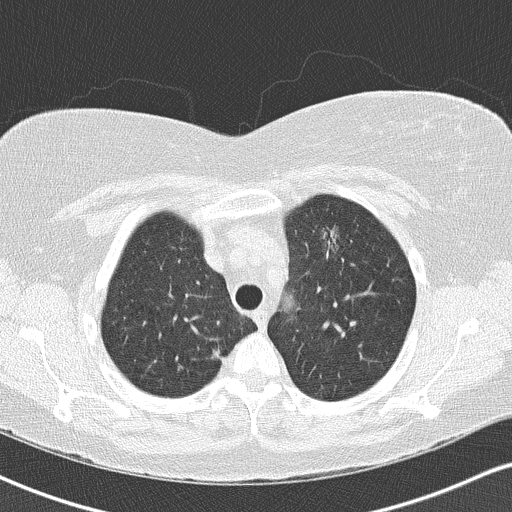
Low-dose screening chest CT, axial slice; second screening round (one year after baseline); lung window (W 1500 / L -600 HU); 120 kVp; slice 116 of 146 in the series. Female participant, aged 57 years at enrolment. Current smoker at enrolment.
Expert-annotated lung lesion, box from (x=311, y=219) to (x=352, y=264) px. The screening reader recorded 3 non-calcified nodules or masses ≥4 mm on this exam (left upper lobe, right upper lobe, right middle lobe); which of them this box marks is not recorded. Official screen result: positive, other. Later outcome: lung cancer diagnosed 75 days after this screen — adenocarcinoma, NOS, left upper lobe, poorly differentiated (G3), stage IA (AJCC 6th edition), 24 mm at pathology.